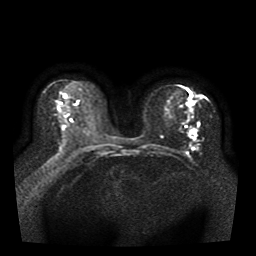
Breast MRI, one axial slice; position 19 of 41 along the scan axis; diffusion-weighted series; image 2 of 4 stored at this slice position (different b-values; order by instance number); 1.5 T; 5 mm slice thickness; 256 × 256 image matrix. Female patient.
Structures marked on this image (expert manual segmentation):
- tumour on diffusion-weighted imaging: bounding box <194,124,200,133> (left, top, right, bottom; pixels)